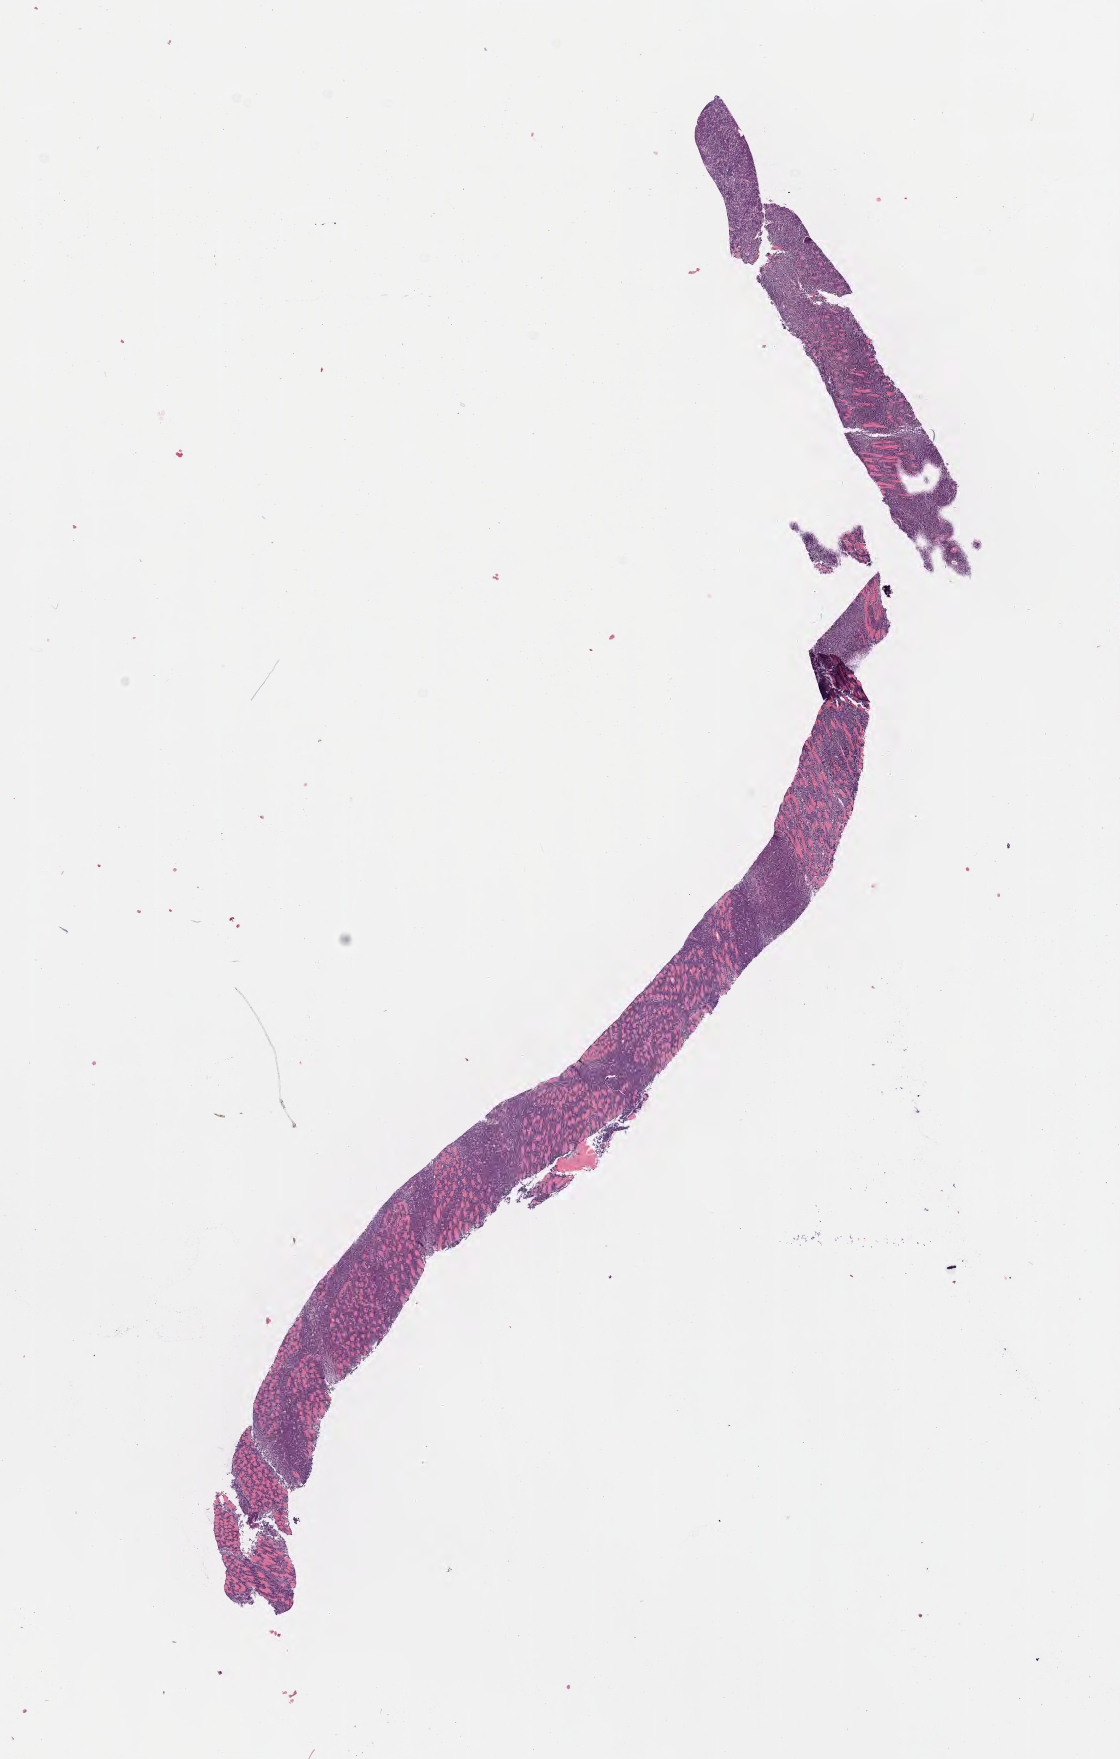
Digitized hematoxylin and eosin (H&E)-stained section — low-resolution overview of the scanned area, about 9.1 x 14.2 mm. Specimen: tumor tissue. Male patient; age at initial diagnosis 4 years.
Histologic diagnosis: Burkitt lymphoma, NOS.